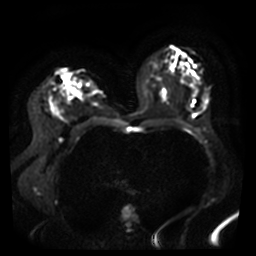
Breast MRI, one axial slice; position 22 of 46 along the scan axis; diffusion-weighted series; image 2 of 4 stored at this slice position (different b-values; order by instance number); 3 T; 5 mm slice thickness; 256 × 256 image matrix, field of view 360 × 360 mm. Female patient.
Annotated regions visible in this slice (outlined manually by an expert reader):
- tumour on diffusion-weighted imaging: bounding box (x1, y1, x2, y2) in pixels: (50, 101, 58, 116)